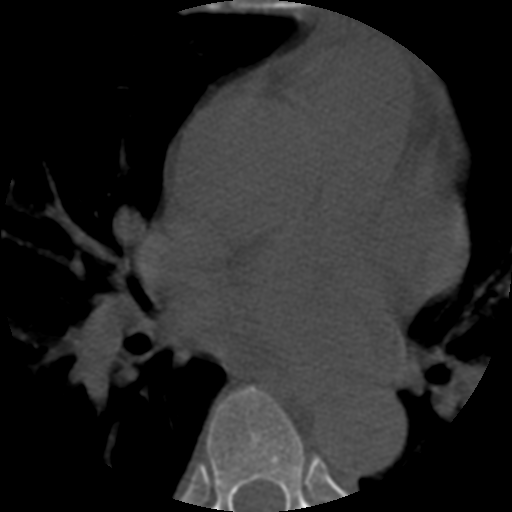
CT including the spine, one axial slice; slice 359 of 508 in the series (ordered by position); reconstruction kernel STANDARD; 120 kVp; bone window (W 1800 / L 400 HU); 1.25 mm slice thickness; 512 × 512 image matrix. Patient age 57 years. Case-level facts recorded for this patient, not image findings: primary cancer: prostate.
Annotated regions visible in this slice (semi-automatically segmented with operator editing):
- T6 vertebra: bounding box [x1, y1, x2, y2] px = [207, 387, 311, 512]